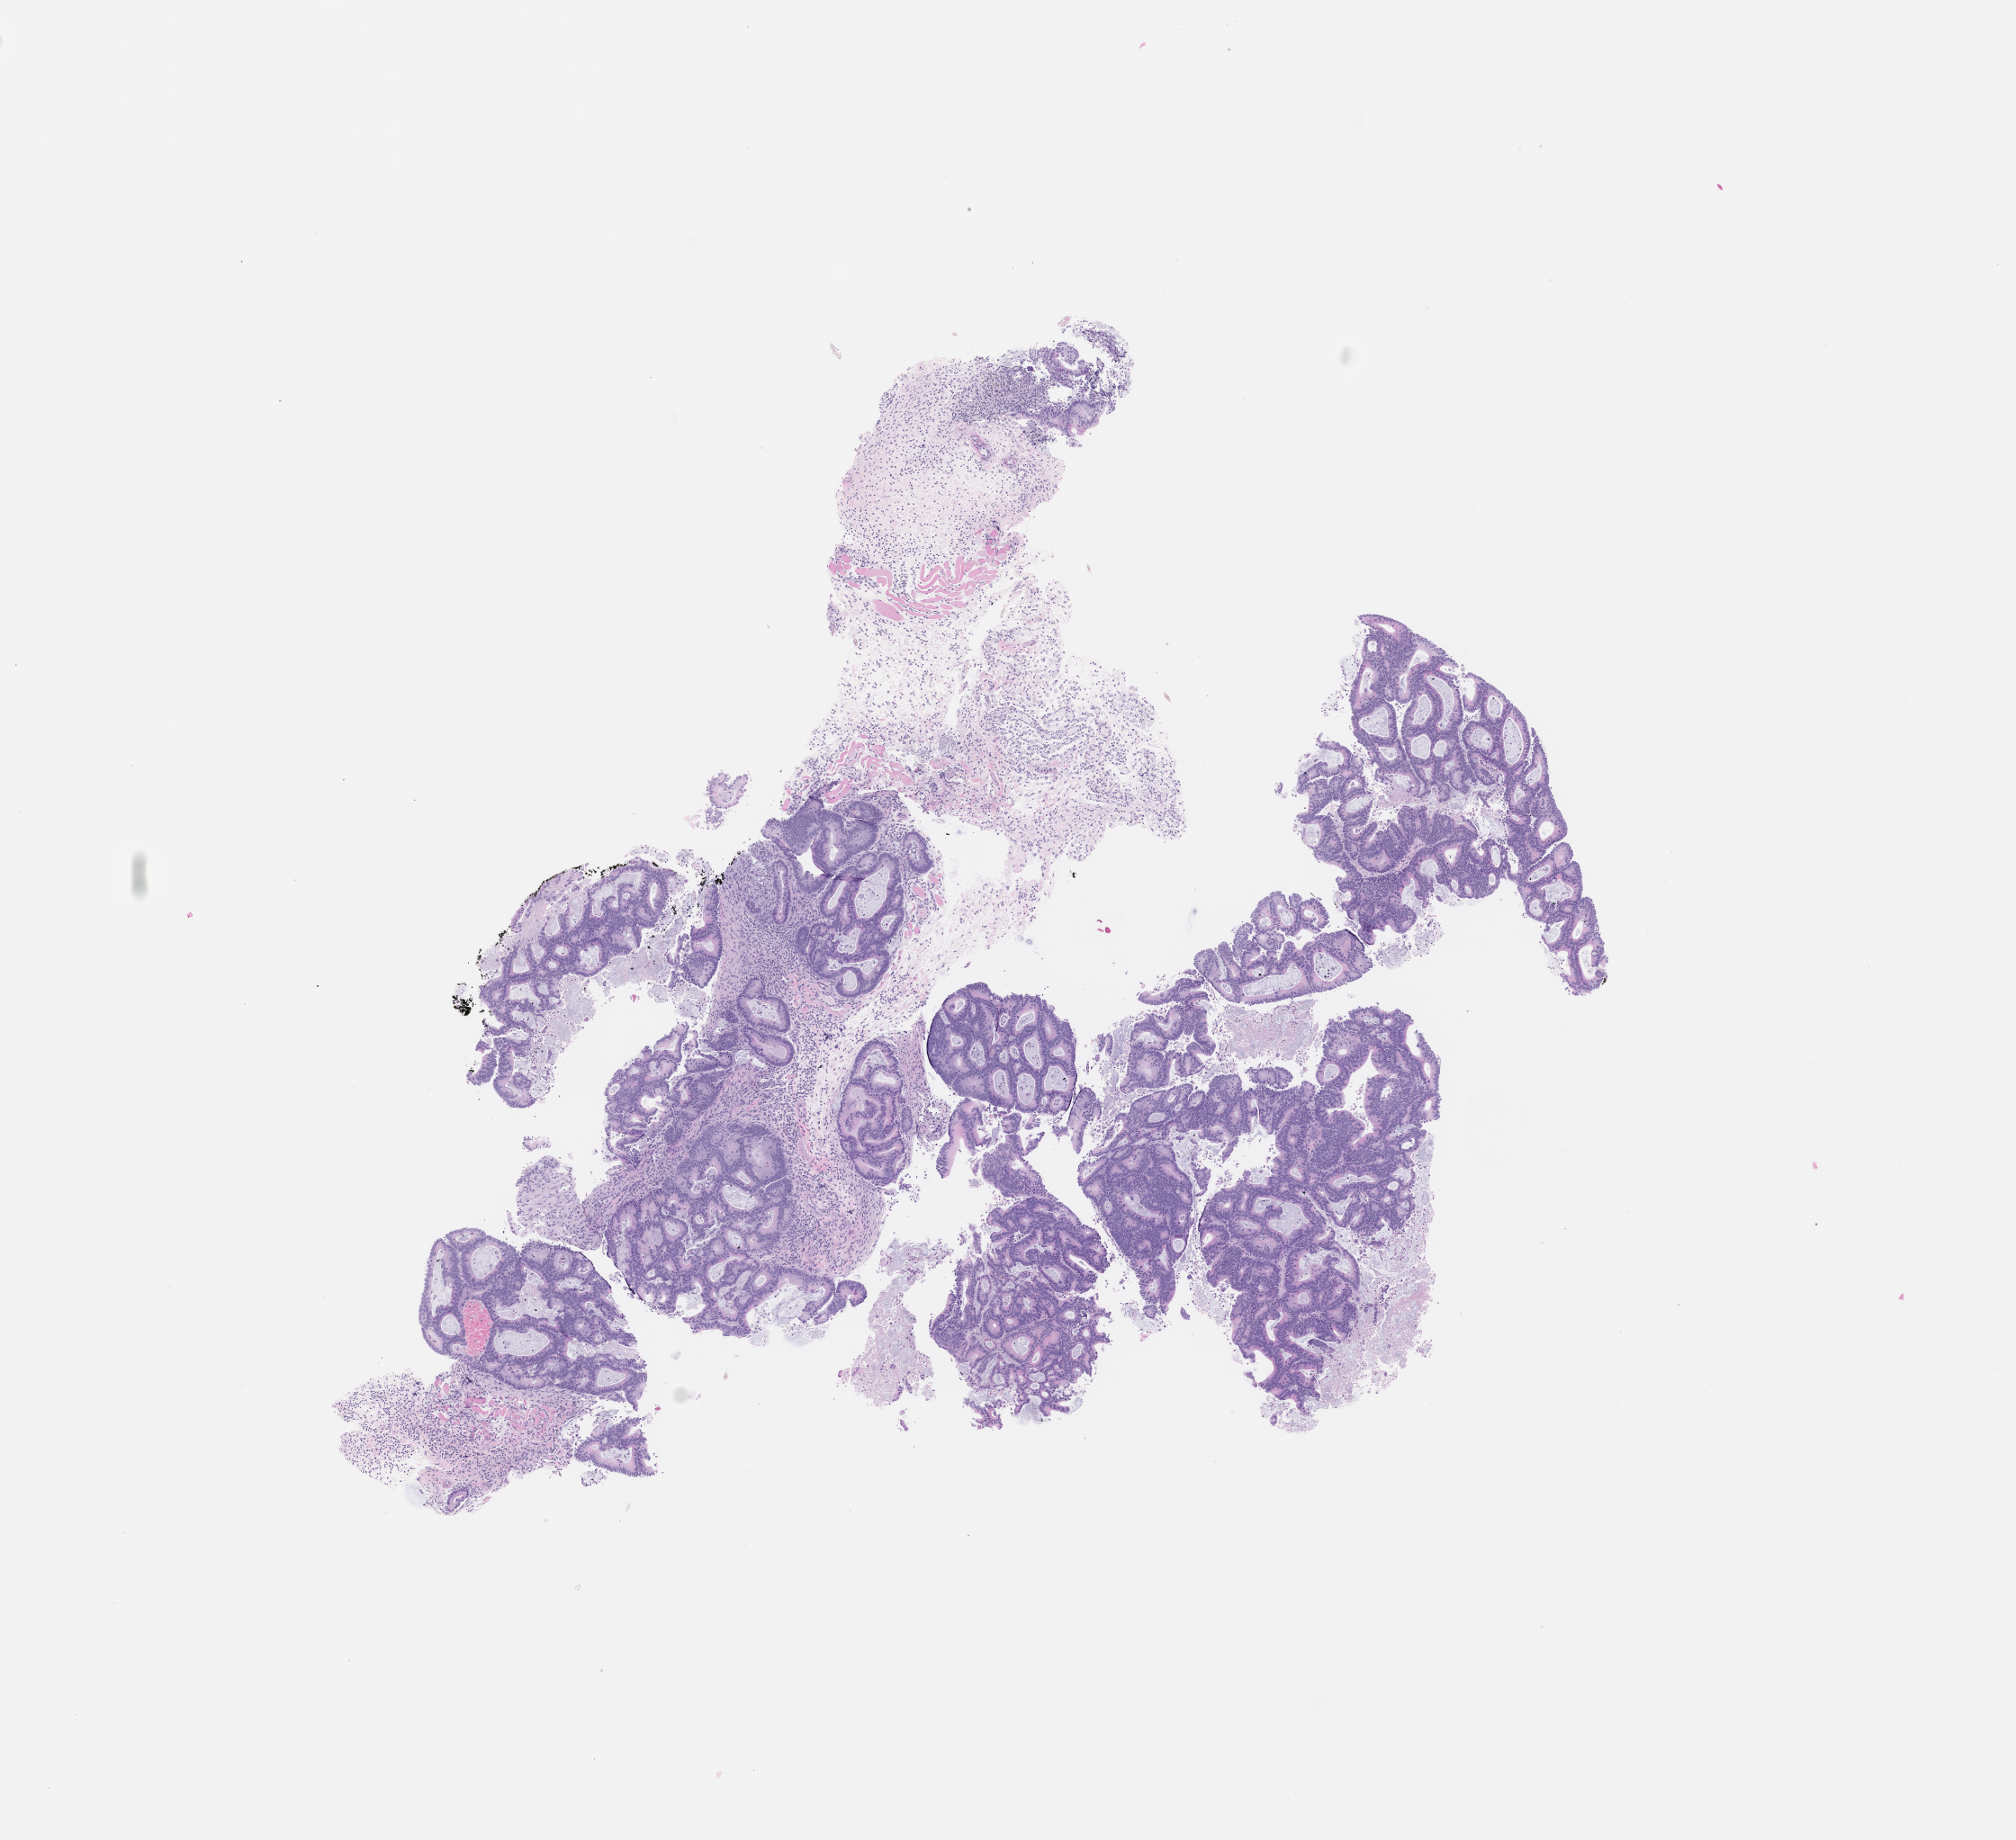
Hematoxylin and eosin (H&E) whole-slide image of a patient-derived xenograft (PDX) tumor grown in a mouse, passage 0 — low-resolution overview of the scanned area, about 9.0 x 8.2 mm; formalin-fixed, paraffin-embedded (FFPE) tissue; originating tumor site category: colon.
Originating patient diagnosis: Colon Adenocarcinoma.